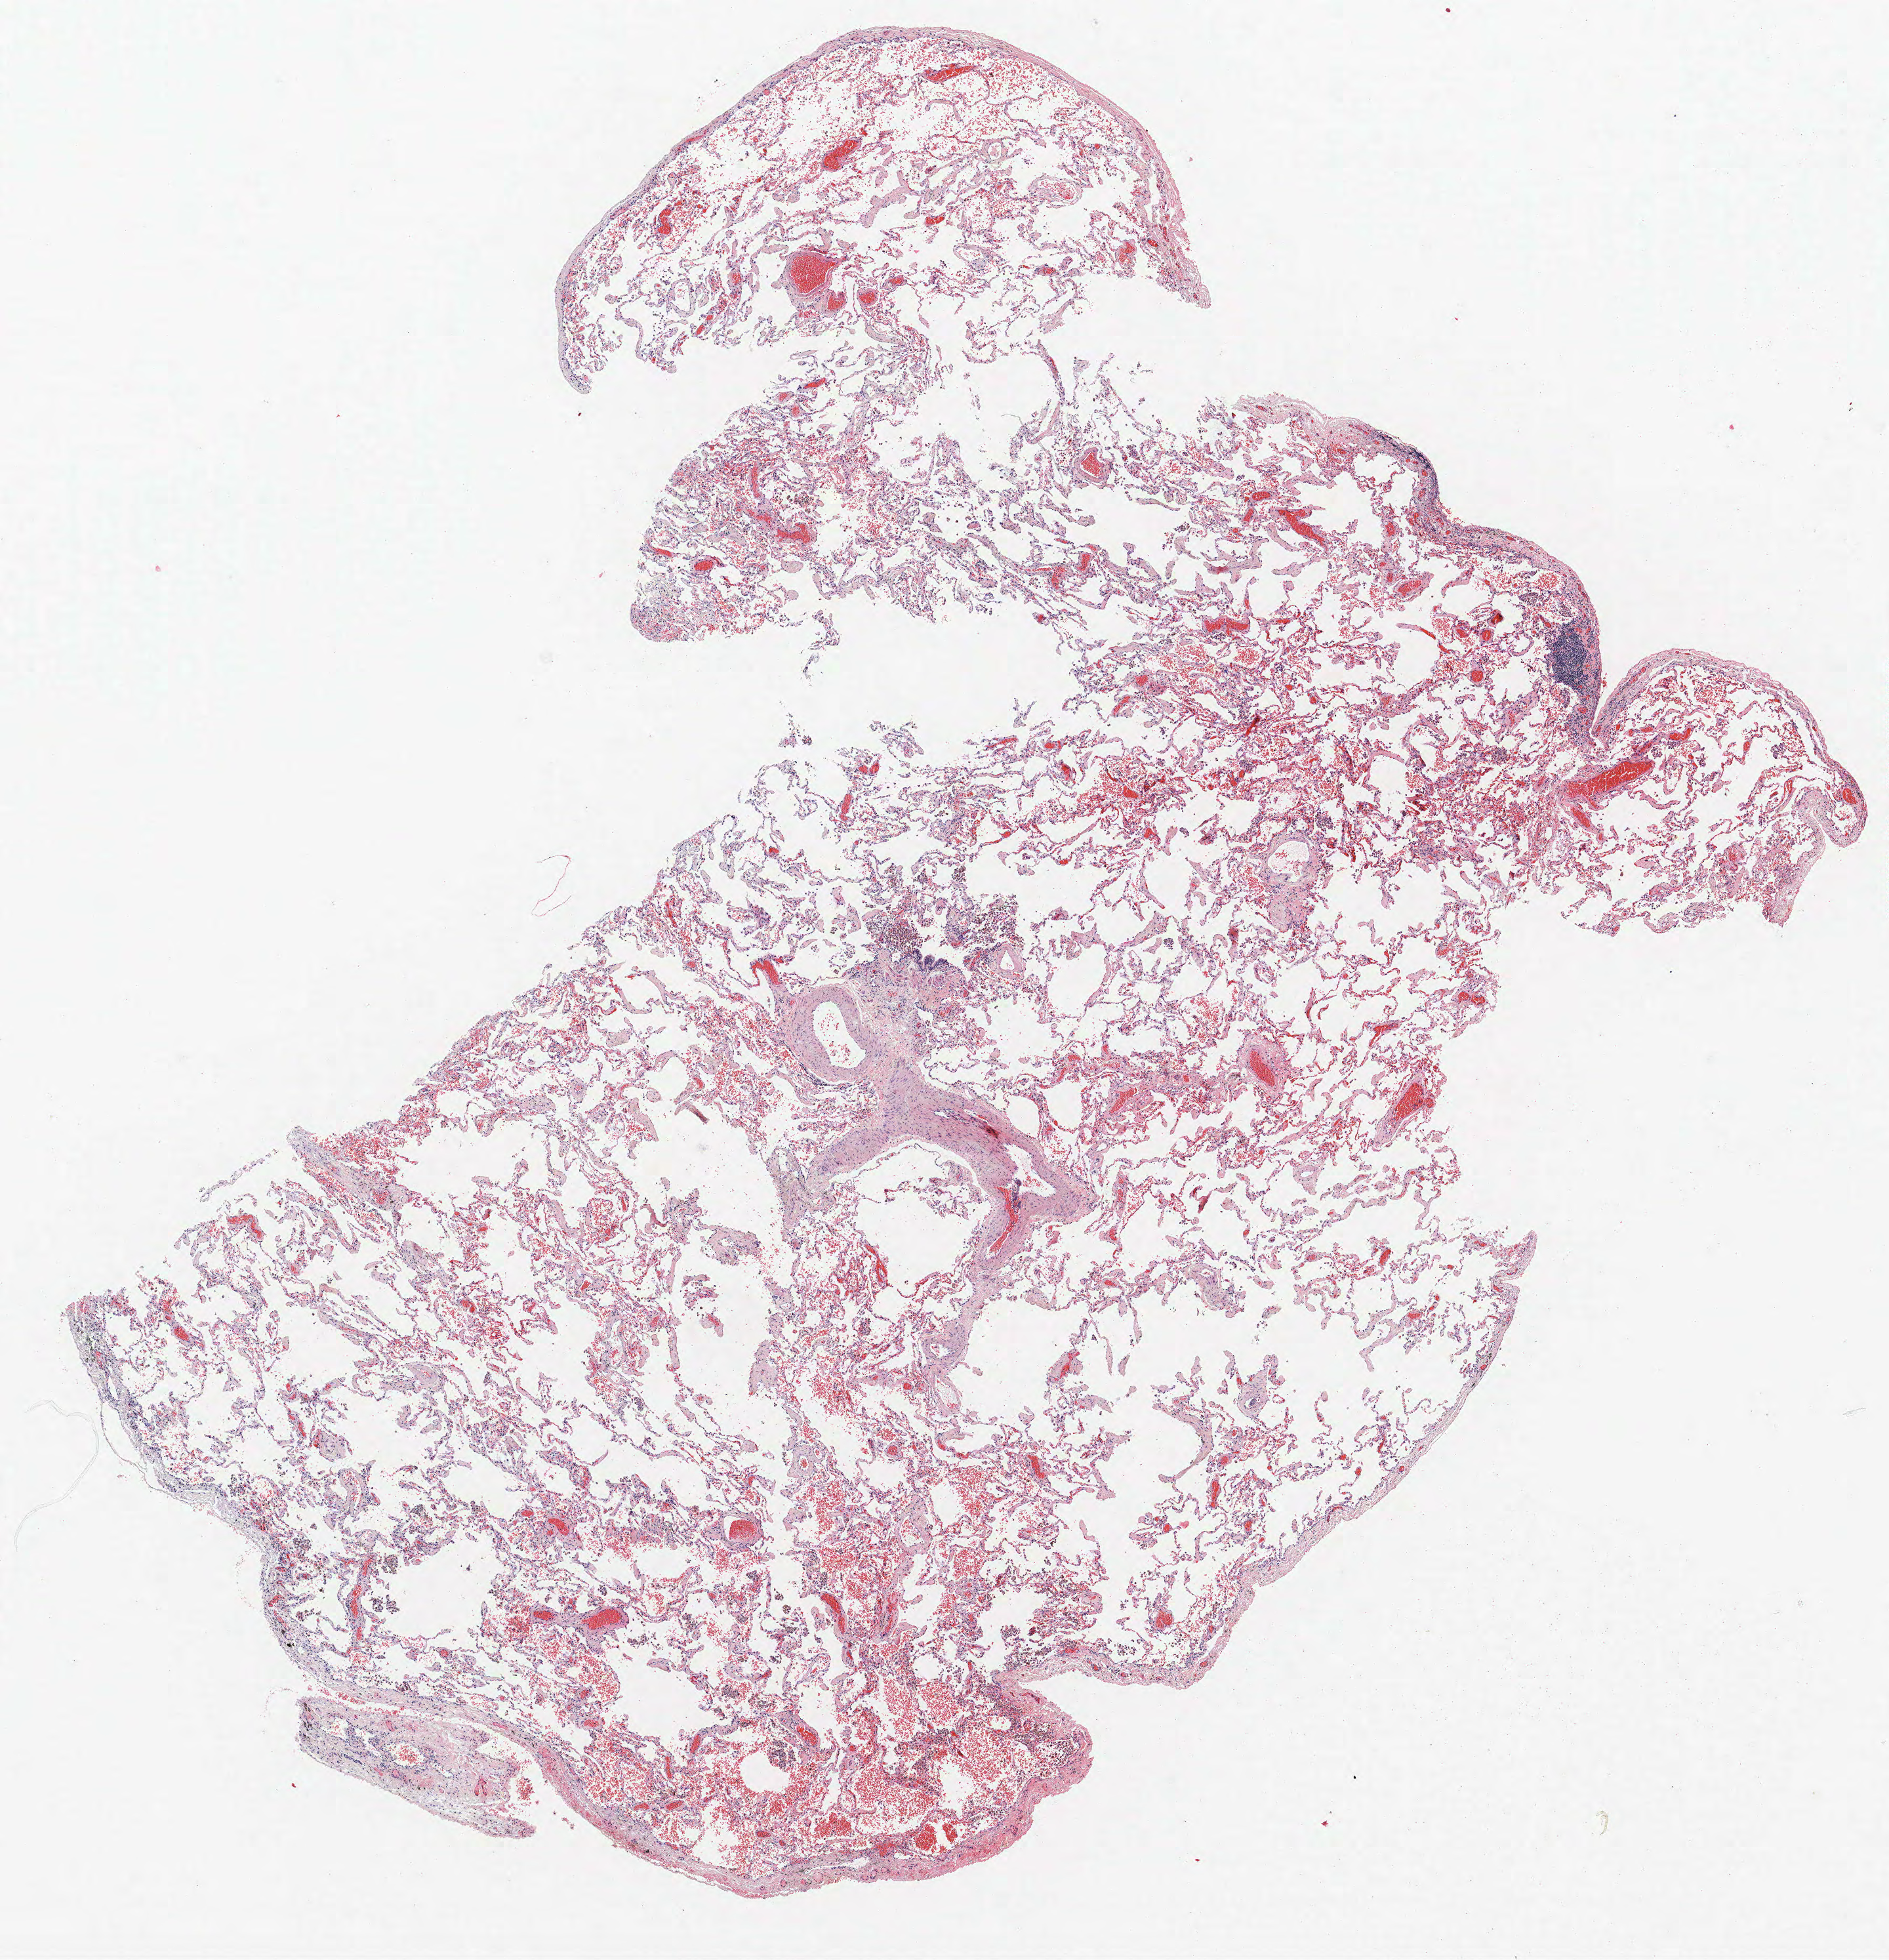
Whole-slide histology image, Hematoxylin and eosin (H&E) stained, a low-resolution overview of the entire scanned area, about 11.5 x 12.0 mm; formalin-fixed paraffin-embedded (FFPE) section; lung tissue. Male, age 70 at enrolment.
Participant's lung-cancer diagnosis: Bronchiolo-alveolar adenocarcinoma, NOS (ICD-O-3 8250/3).